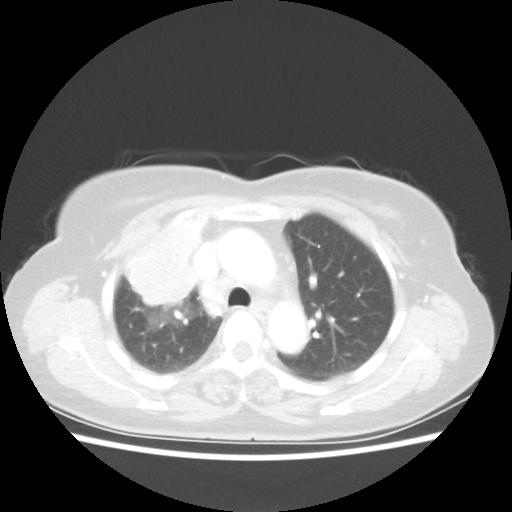
Chest CT, one axial slice. Slice 38 of 55 in the series (ordered by position). Lung window (W 1500 / L -600 HU). 5 mm slice thickness. 512 × 512 image matrix, field of view 337 × 337 mm. Female patient, age 62 years. From the clinical record (not read from this slice): clinical TNM (as recorded): T4 N3 M0.
Structures marked on this image (rectangle marked by the reading radiologist):
- lung tumour (recorded histology: squamous cell carcinoma): bounding box (x1, y1, x2, y2) in pixels: (116, 203, 212, 314)